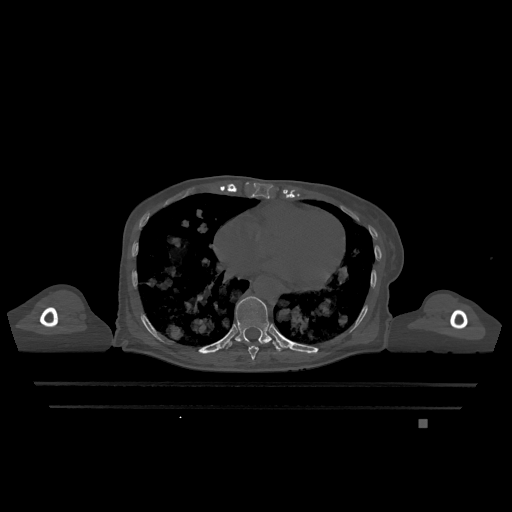
CT including the spine, one axial slice. Slice 662 of 1317 in the series (ordered by position). Bone window (W 1800 / L 400 HU). 0.5 mm slice thickness. 512 × 512 image matrix, field of view 500 × 500 mm. Female patient, age 74 years. Case-level facts recorded for this patient, not image findings: primary cancer: lung; vertebrae with lytic lesions (as recorded): T1, T4, T5, T6, L4, L5.
Annotated regions visible in this slice (semi-automatic segmentation, software-assisted and operator-edited):
- T10 vertebra: box from (x=226, y=296) to (x=282, y=352) px
- T9 vertebra: (x=248, y=345)–(x=259, y=360)